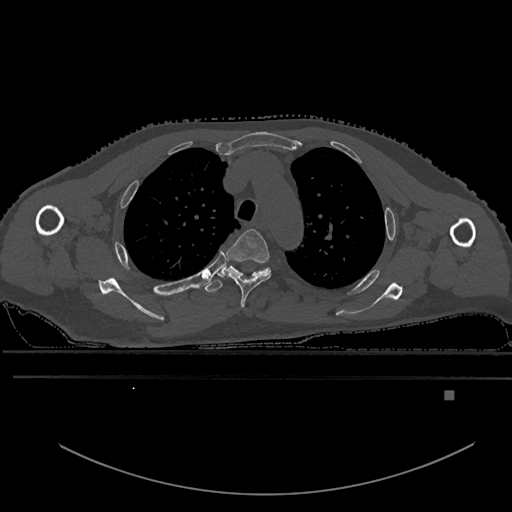
CT including the spine, one axial slice; slice 437 of 969 in the series (ordered by position); bone window (W 1800 / L 400 HU); 0.5 mm slice thickness; 512 × 512 image matrix, field of view 456 × 456 mm. Male patient, age 82 years. Case-level facts recorded for this patient, not image findings: primary cancer: prostate; vertebrae with lytic lesions (as recorded): T11, T9, T8, T2.
Annotated regions visible in this slice (semi-automatic segmentation, software-assisted and operator-edited):
- T3 vertebra: bounding box <221,229,272,308> (left, top, right, bottom; pixels)
- T4 vertebra: <204,263,271,293>